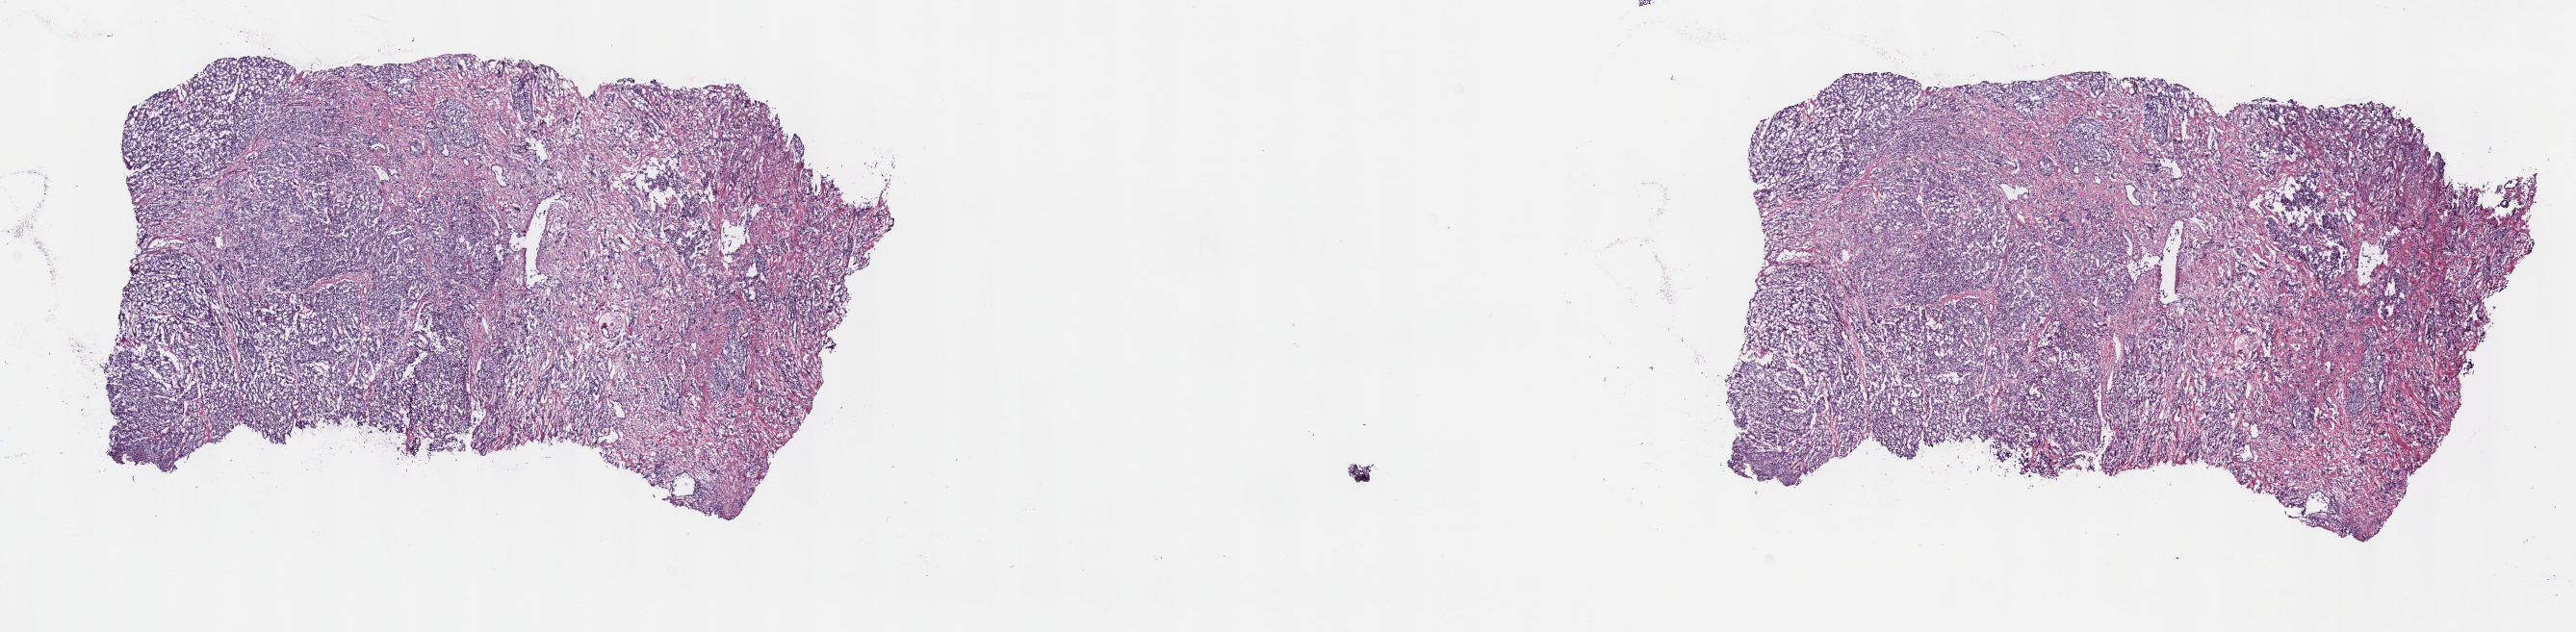
Digitized Hematoxylin and eosin (H&E) stained tissue section (whole slide), shown as a low-resolution overview of the whole scanned area (about 21.6 x 5.3 mm, from a 40x scan), frozen section from the top of the tissue portion, primary tumour sample from the prostate. Male, age 51 years at initial diagnosis. Gleason score: 9 (5+4). Composition of this section per pathologist review: tumour cells 80%, tumour nuclei 90%, normal cells 20%, stromal cells 0%, necrosis 0%. Inflammatory infiltration, as recorded: lymphocyte infiltration 0%, monocyte infiltration 0%, neutrophil infiltration 0%.
Pathologic diagnosis: Adenocarcinoma, NOS (prostate gland). Lymph nodes positive (case pathology): 2 of 22 examined.